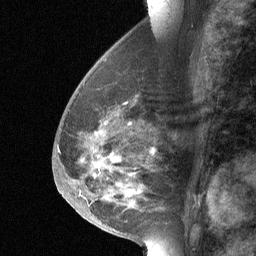
Breast MRI (dynamic contrast-enhanced), one sagittal slice. Position 29 of 64 along the scan axis. Dynamic contrast-enhanced study with each time point stored as its own series, time point 2 of 3 at this slice position (early post-contrast, ordered by acquisition time). 1.5 T. TE 4.8 ms, TR 27 ms. 256 × 256 image matrix, field of view 180 × 180 mm. Patient: female, 56 years. Case-level facts recorded for this patient, not image findings: setting: breast cancer imaged before/during neoadjuvant chemotherapy; receptor status: HER2-positive.
Structures marked on this image (semi-automatic segmentation, software-assisted and operator-edited):
- analysis volume of interest (the breast-tissue region the enhancement analysis was run in; not a lesion): bounding box [x1, y1, x2, y2] px = [68, 83, 164, 214]
- tumour enhancement mask (voxels above the 90 % enhancement threshold inside the analysis volume of interest): [114, 157, 133, 193]